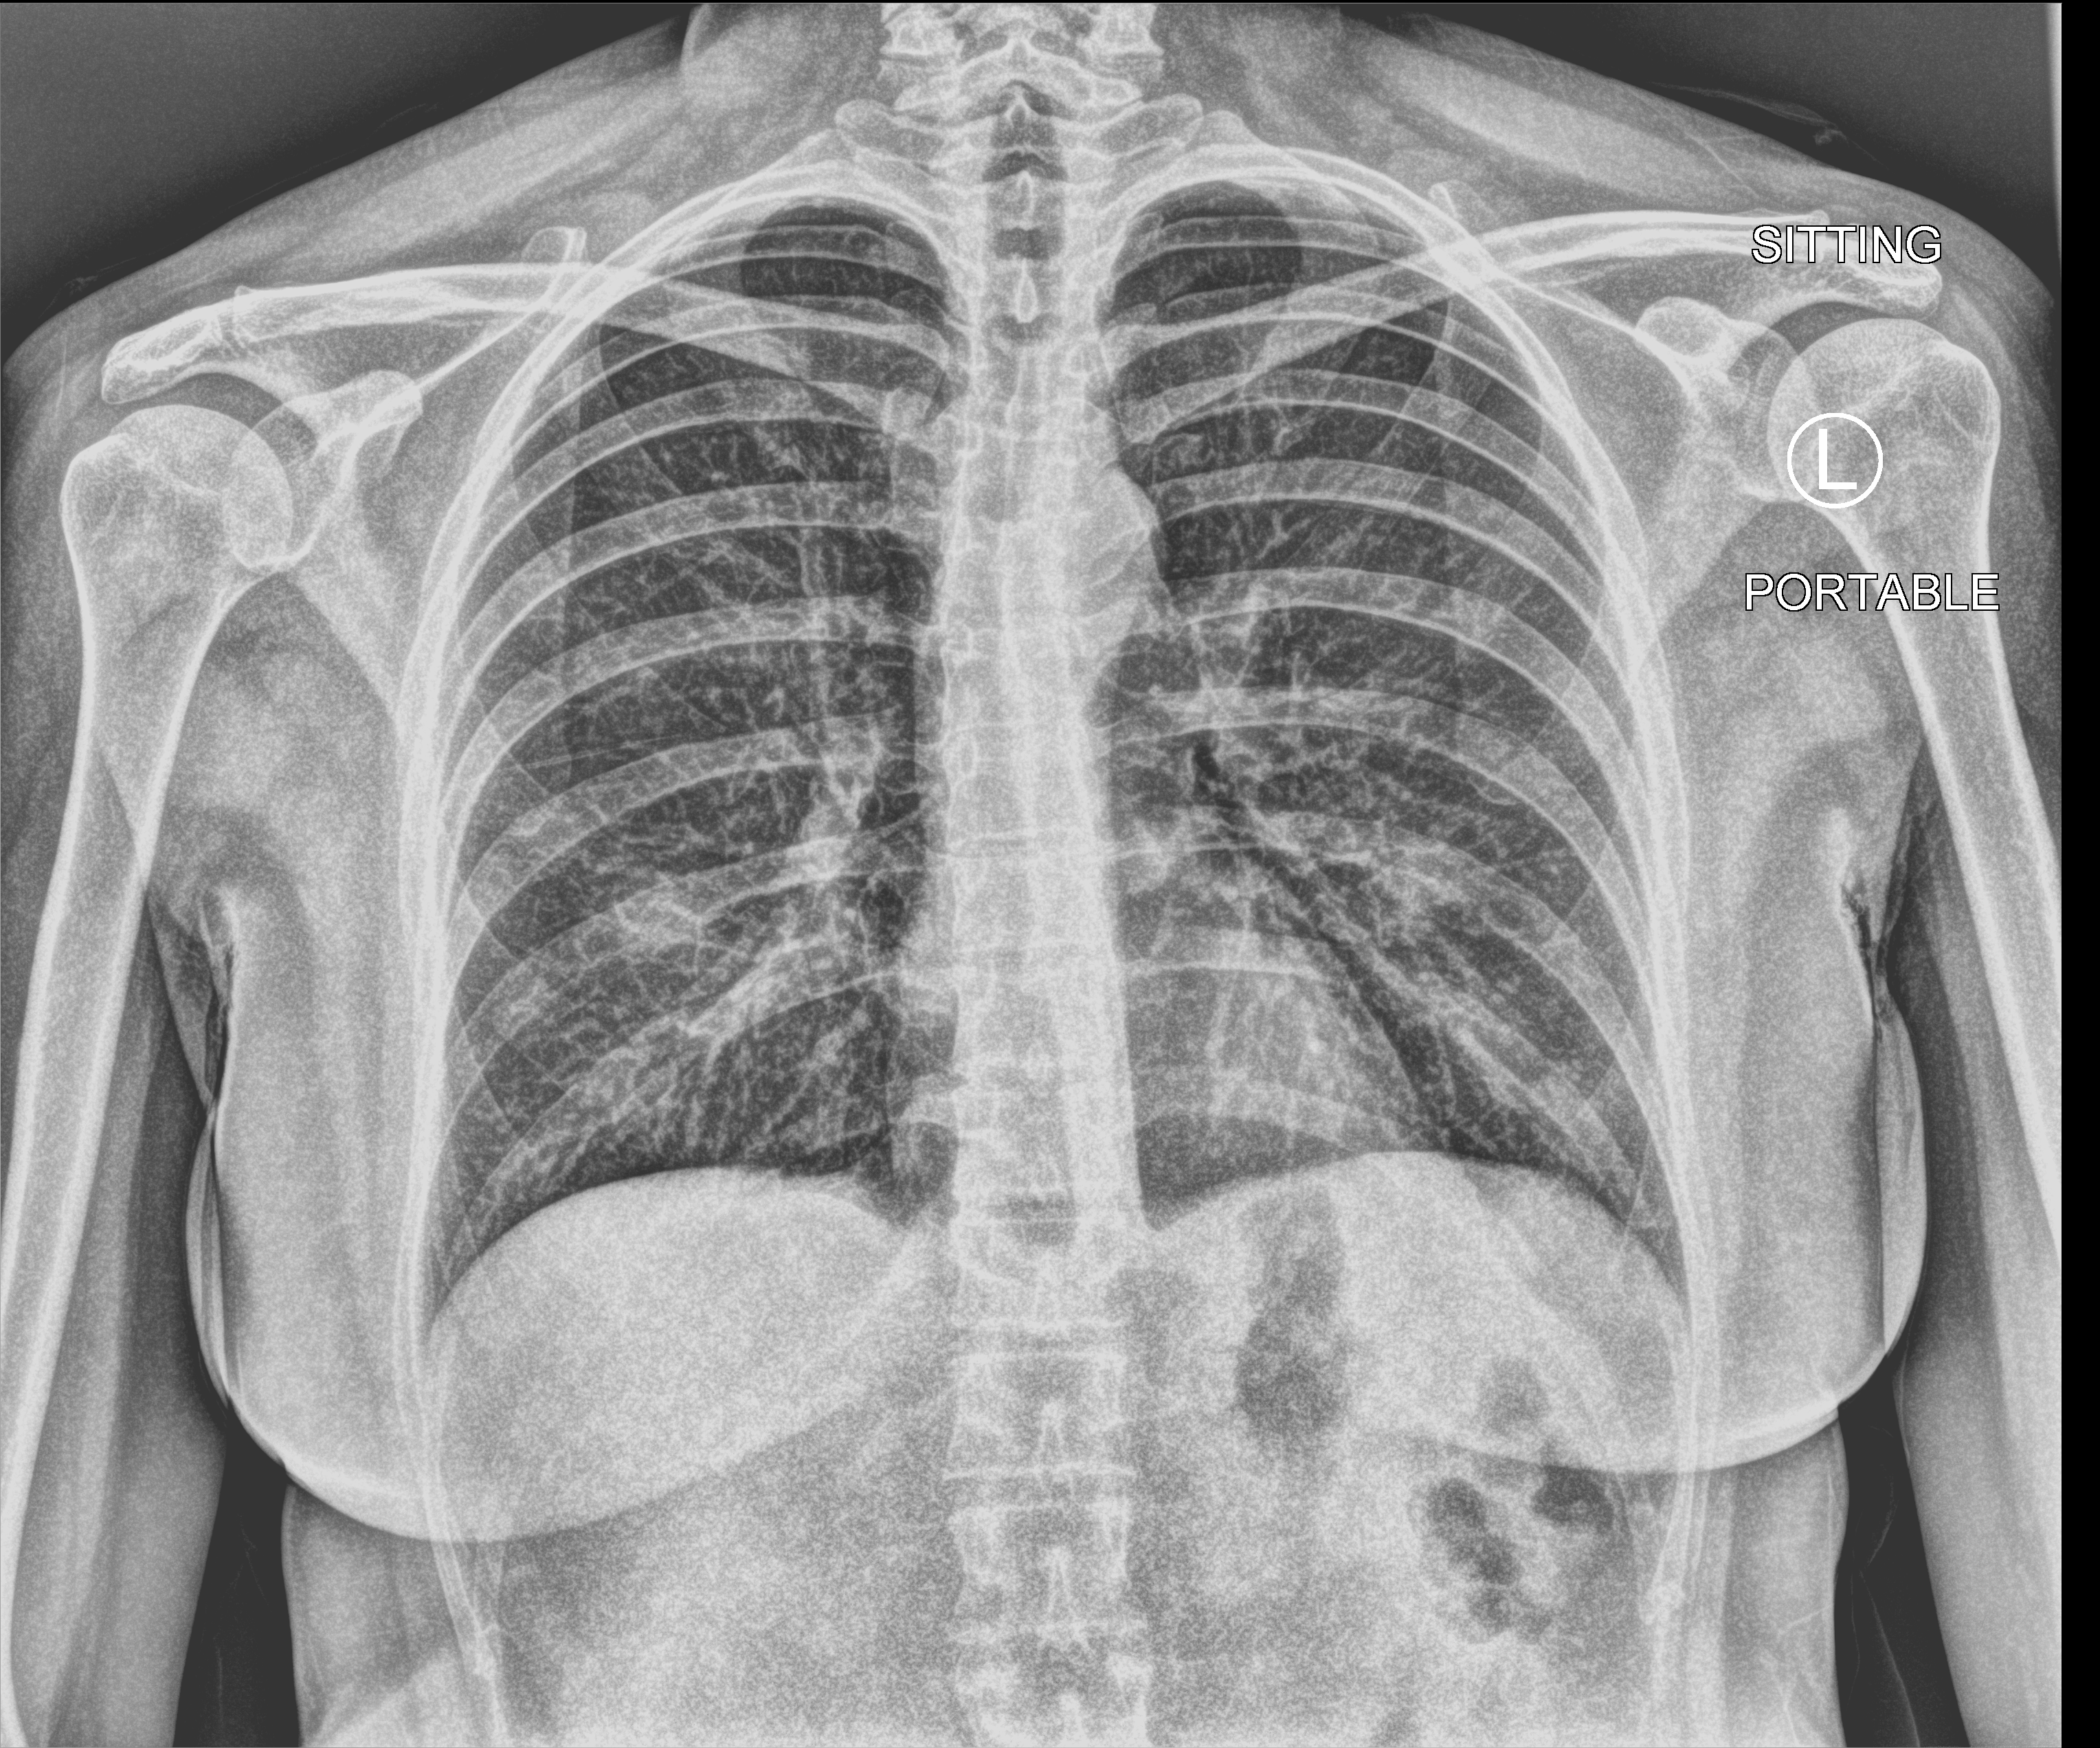
Chest X-ray (portable), anteroposterior (AP) projection. Female patient hospitalised with COVID-19, age 18–59 years.
Hospital-stay facts (about this admission, not read from this image; timing relative to this image not recorded): mechanically ventilated during this hospital stay: no; admitted to intensive care during this hospital stay: no; length of hospital stay: 1 day.